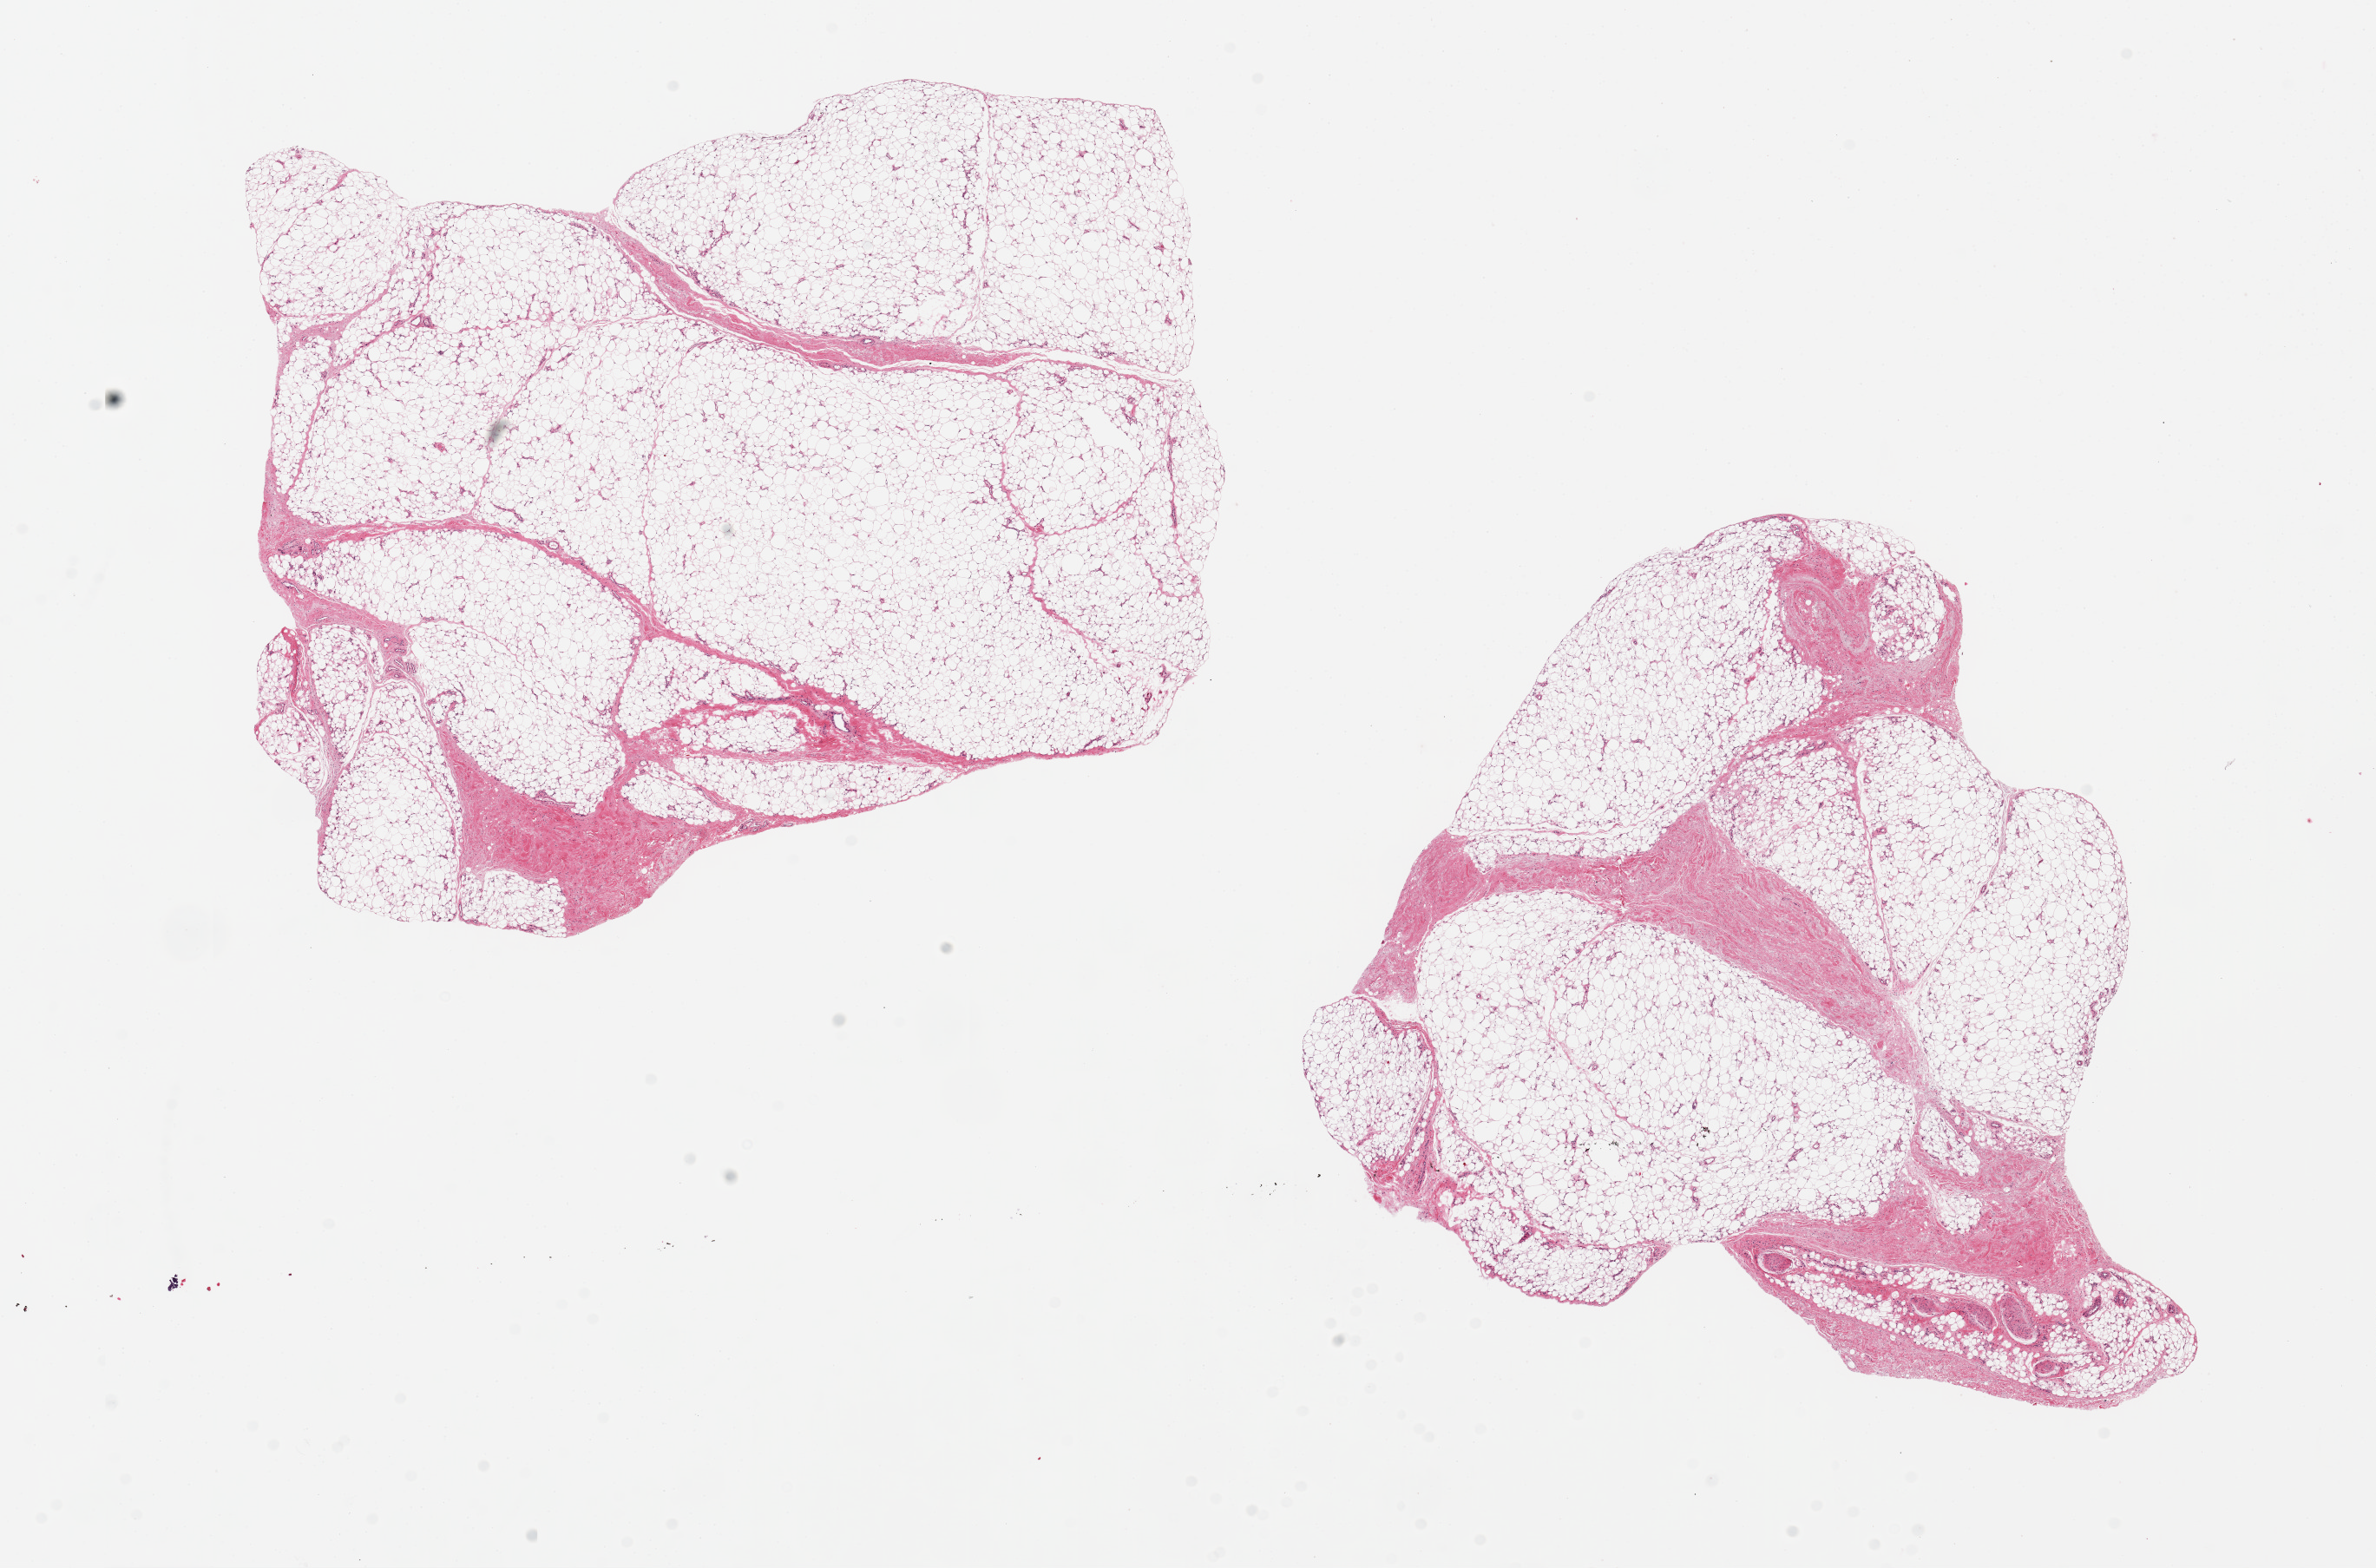
Whole-slide image, H&E stain — a low-resolution overview of the entire scanned area, about 21.7 x 14.3 mm. PAXgene-fixed paraffin-embedded (PFPE) section. Sampled site (target tissue): adipose tissue. Tissue donor sample. Donor: male.
Review note (as recorded): 2 pieces 9x8 & 9x8mm; ~30% fibrostic.